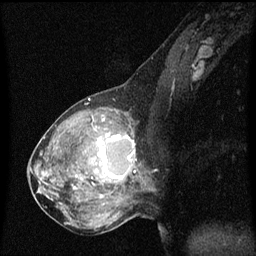
Breast MRI (dynamic contrast-enhanced), one sagittal slice. Position 29 of 60 along the scan axis. Dynamic contrast-enhanced series, image 2 of 3 at this slice position (ordered by acquisition). 1.5 T. TE 4.2 ms, TR 8 ms. 2 mm slice thickness. 256 × 256 image matrix, field of view 200 × 200 mm. Patient: female, 50 years.
Outlined on this slice (semi-automatic segmentation, software-assisted and operator-edited):
- analysis volume of interest (the breast-tissue region the enhancement analysis was run in; not a lesion): box from (x=91, y=126) to (x=141, y=189) px
- tumour enhancement mask (voxels above the 70 % enhancement threshold inside the analysis volume of interest): (x=92, y=134)–(x=135, y=179)